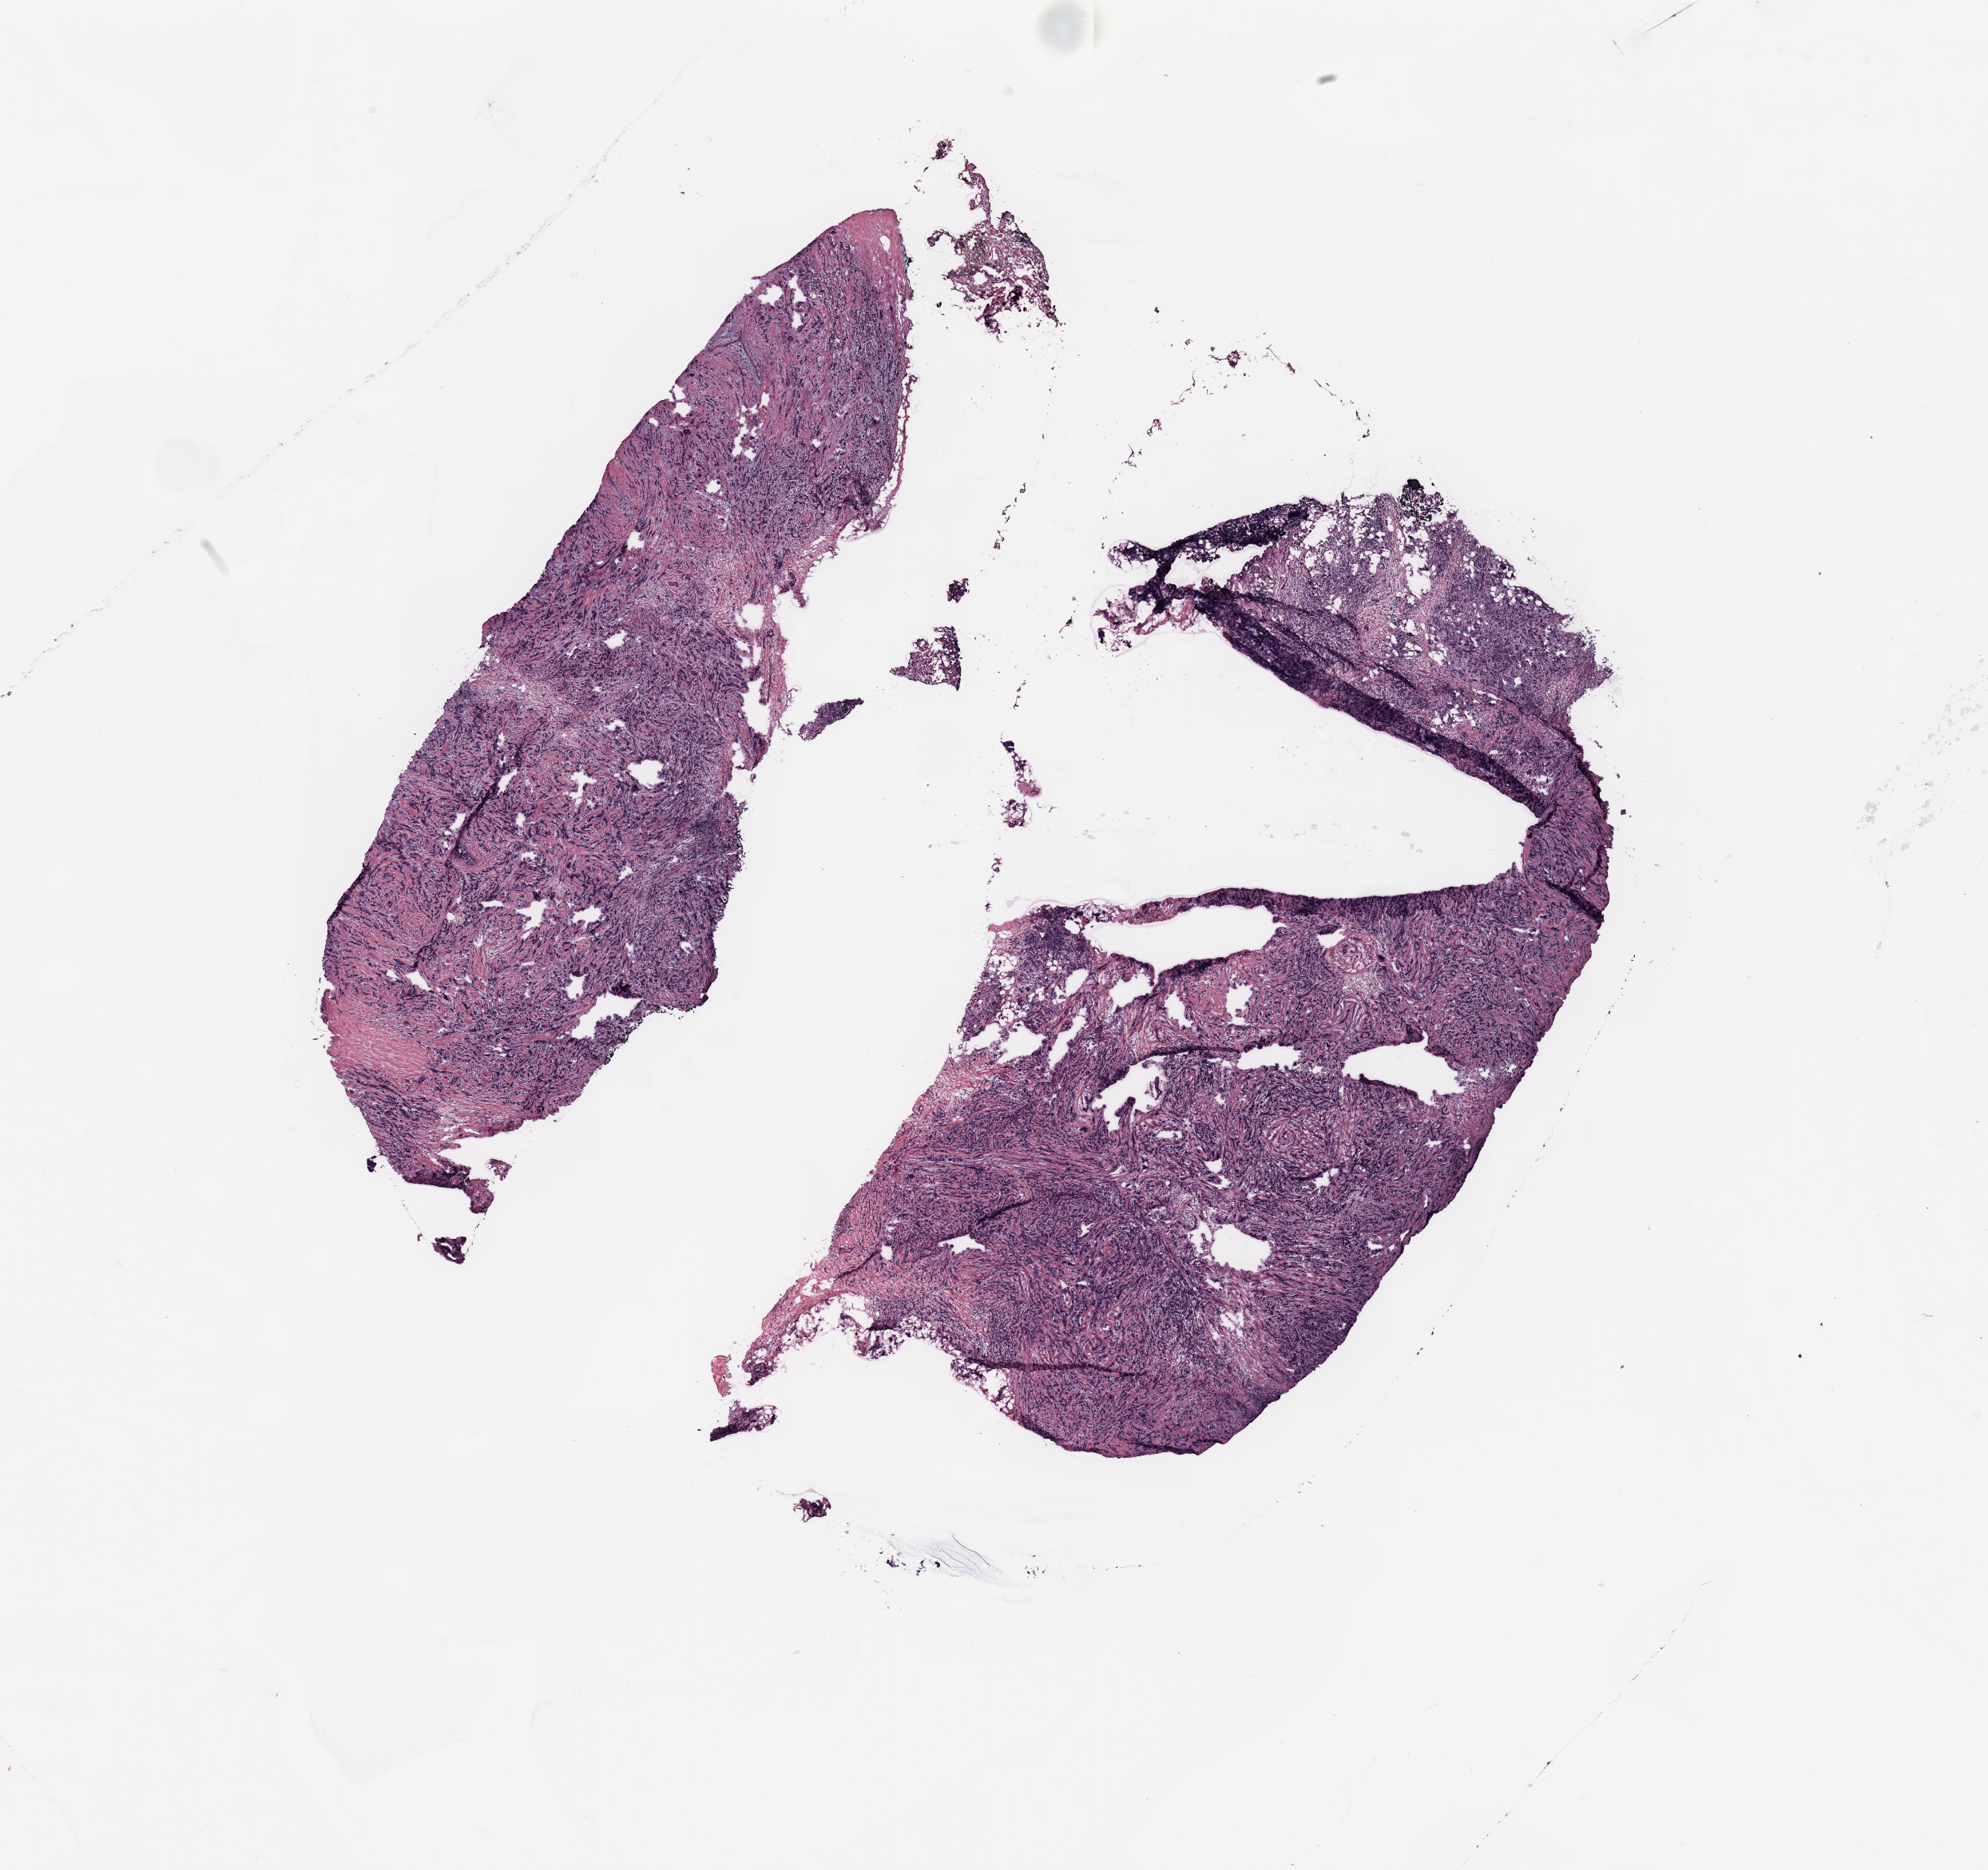
Digitized H&E tissue section (whole slide) — a low-resolution overview of the entire scanned area, about 19.7 x 18.5 mm (slide scanned at 20x); breast, tissue type not recorded.
Patient diagnosis (cohort enrolment): breast cancer (breast).